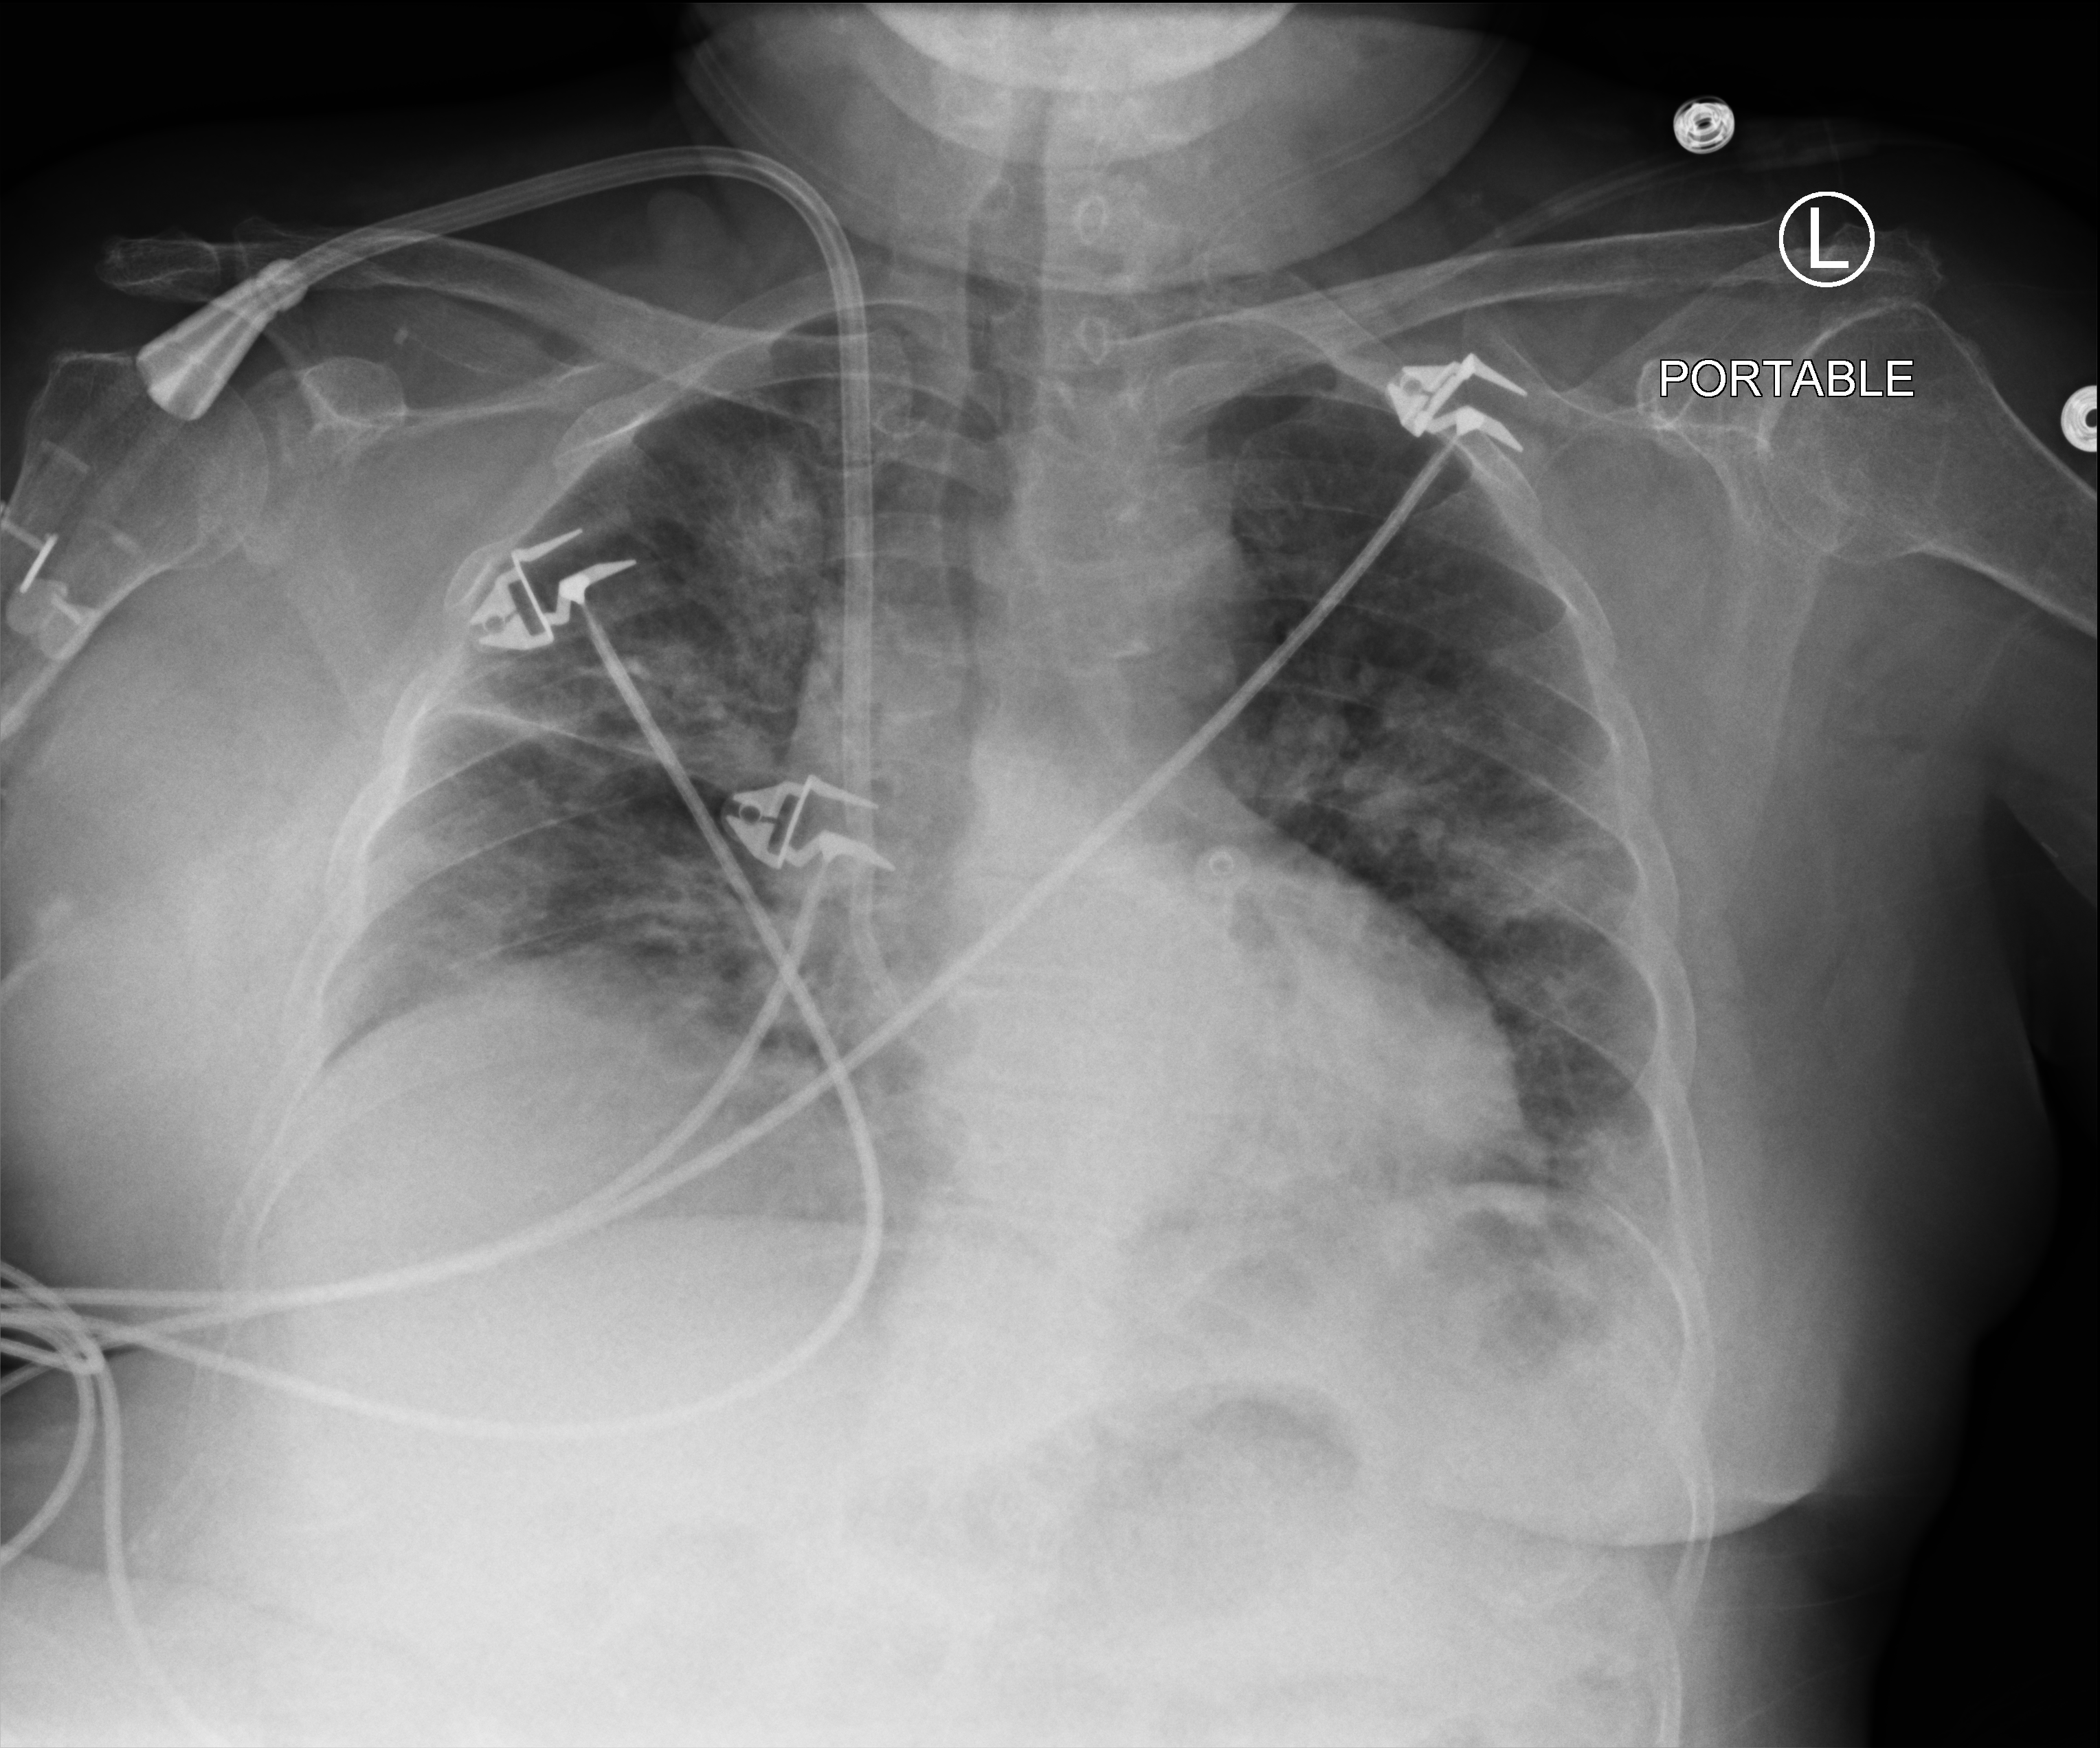
Portable chest radiograph, anteroposterior (AP) projection. Female patient hospitalised with COVID-19, age 60–74 years.
Hospital-stay facts (about this admission, not read from this image; timing relative to this image not recorded):
- hypertension (admission record): yes